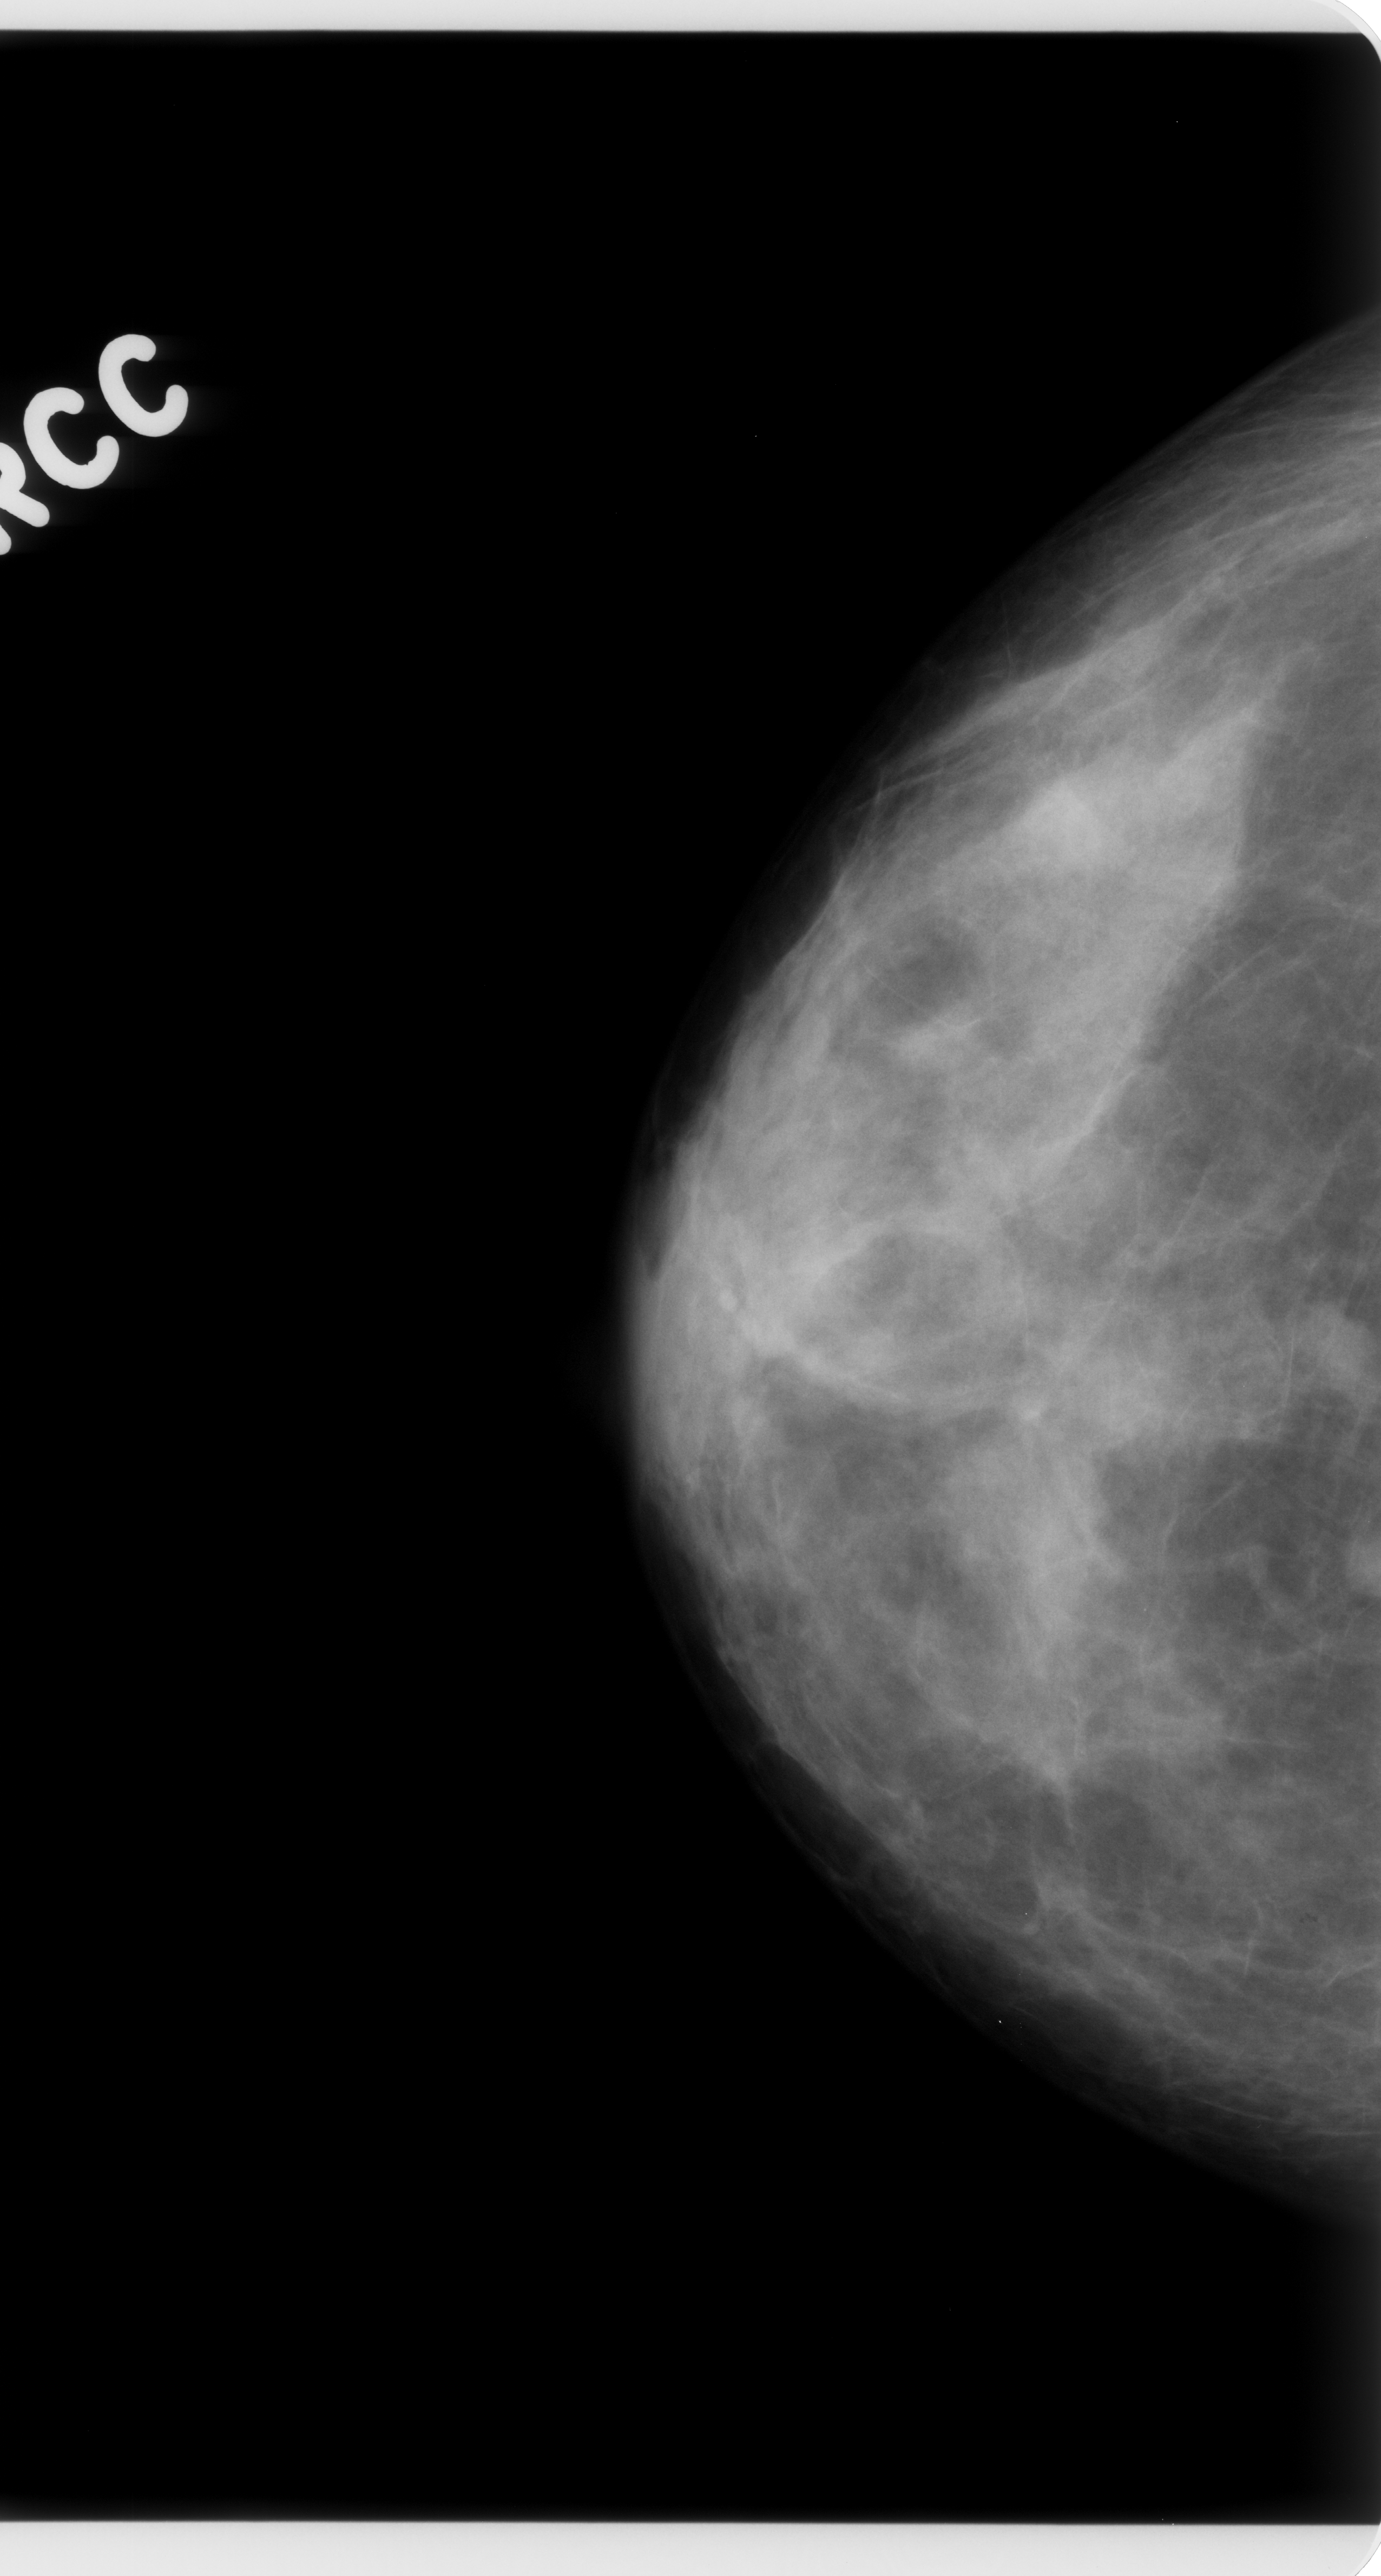
Mammogram (digitized film); right breast; craniocaudal (CC) view; breast composition: scattered fibroglandular densities (BI-RADS density category 2 of 4); 1381 × 2576 image matrix.
Expert-marked regions of interest on this image (one box per marked abnormality):
- mass, shape round, margins circumscribed; BI-RADS assessment category 4; pathology result (as recorded, not read from the image): malignant: bounding box (x1, y1, x2, y2) in pixels: (1340, 1531, 1371, 1596)